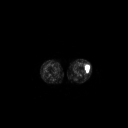
FDG PET of an extremity soft-tissue mass (from a PET/CT study), one axial slice; position 170 of 223 along the scan axis; 128 × 128 image matrix, field of view 700 × 700 mm. Patient: female, 16 years. Case-level facts recorded for this patient, not image findings: histological type: spindle cell suggestive of biphasic synovial sarcoma; grade: intermediate; site of the primary tumour: left knee.
Annotated regions visible in this slice (expert contour drawn on MRI and transferred to this co-registered scan by the dataset authors):
- gross tumour volume including surrounding oedema: bounding box <85,63,90,73> (left, top, right, bottom; pixels)
- gross tumour volume (mass): <85,64,90,73>